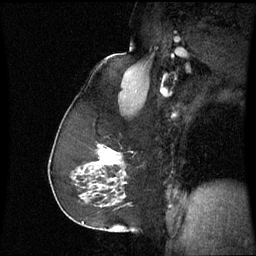
Breast MRI (dynamic contrast-enhanced), one sagittal slice. Position 39 of 60 along the scan axis. Dynamic contrast-enhanced series, image 2 of 3 at this slice position (ordered by acquisition). 1.5 T. TE 4.2 ms, TR 8.9 ms. 256 × 256 image matrix, field of view 220 × 220 mm. Patient: female, 59 years. Case-level facts recorded for this patient, not image findings: setting: breast cancer imaged before/during neoadjuvant chemotherapy; receptor status: triple-negative.
Structures marked on this image (semi-automatically segmented with operator editing):
- analysis volume of interest (the breast-tissue region the enhancement analysis was run in; not a lesion): bounding box (x1, y1, x2, y2) in pixels: (88, 144, 127, 197)
- tumour enhancement mask (voxels above the 70 % enhancement threshold inside the analysis volume of interest): (100, 152, 119, 165)